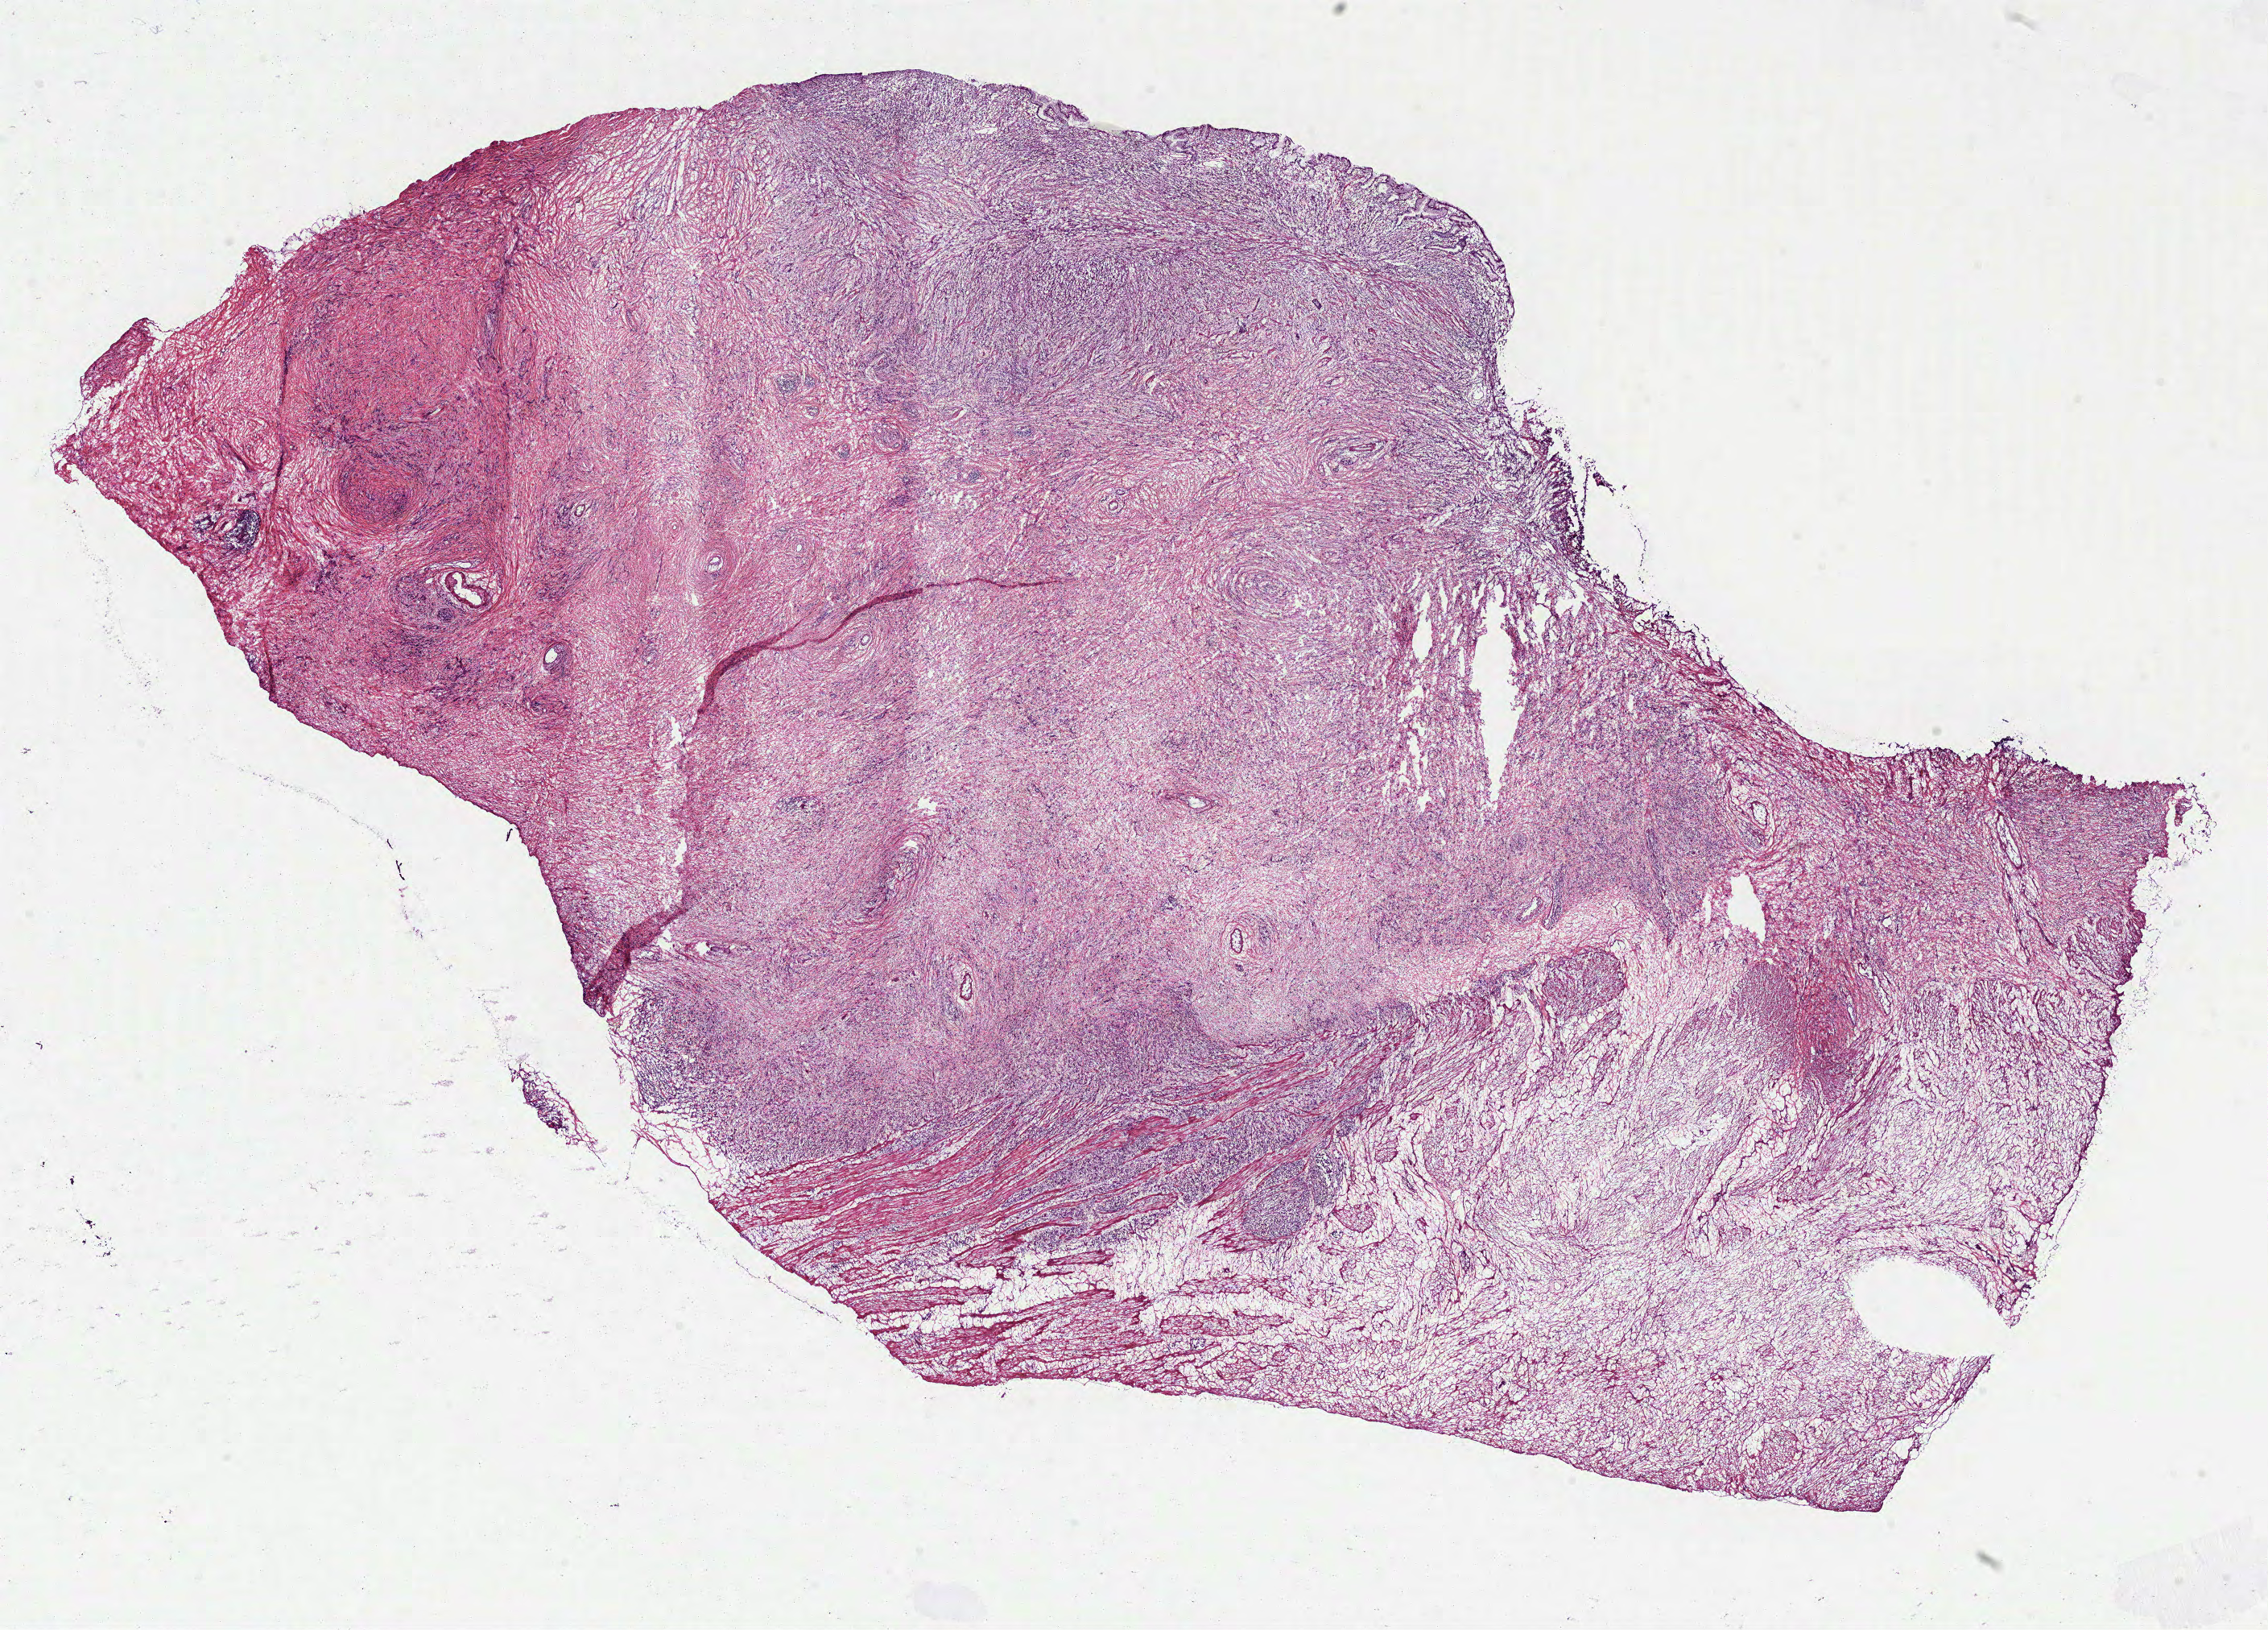
Whole-slide histology image, H&E, shown as a low-resolution overview of the whole scanned area (about 22.7 x 16.3 mm), frozen section from the bottom of the tissue portion, primary tumour sample from the stomach. Female, age 50 years at initial diagnosis. Histologic grade: GX (grade cannot be assessed). Pathologist review of this section (percent, as recorded): tumour cells 45%, tumour nuclei 60%, normal cells 5%, stromal cells 50%, necrosis 0%.
• AJCC pathologic stage: IV (7th edition)
• histologic diagnosis: Adenocarcinoma, intestinal type
• lymph nodes positive (case pathology): 7 of 8 examined